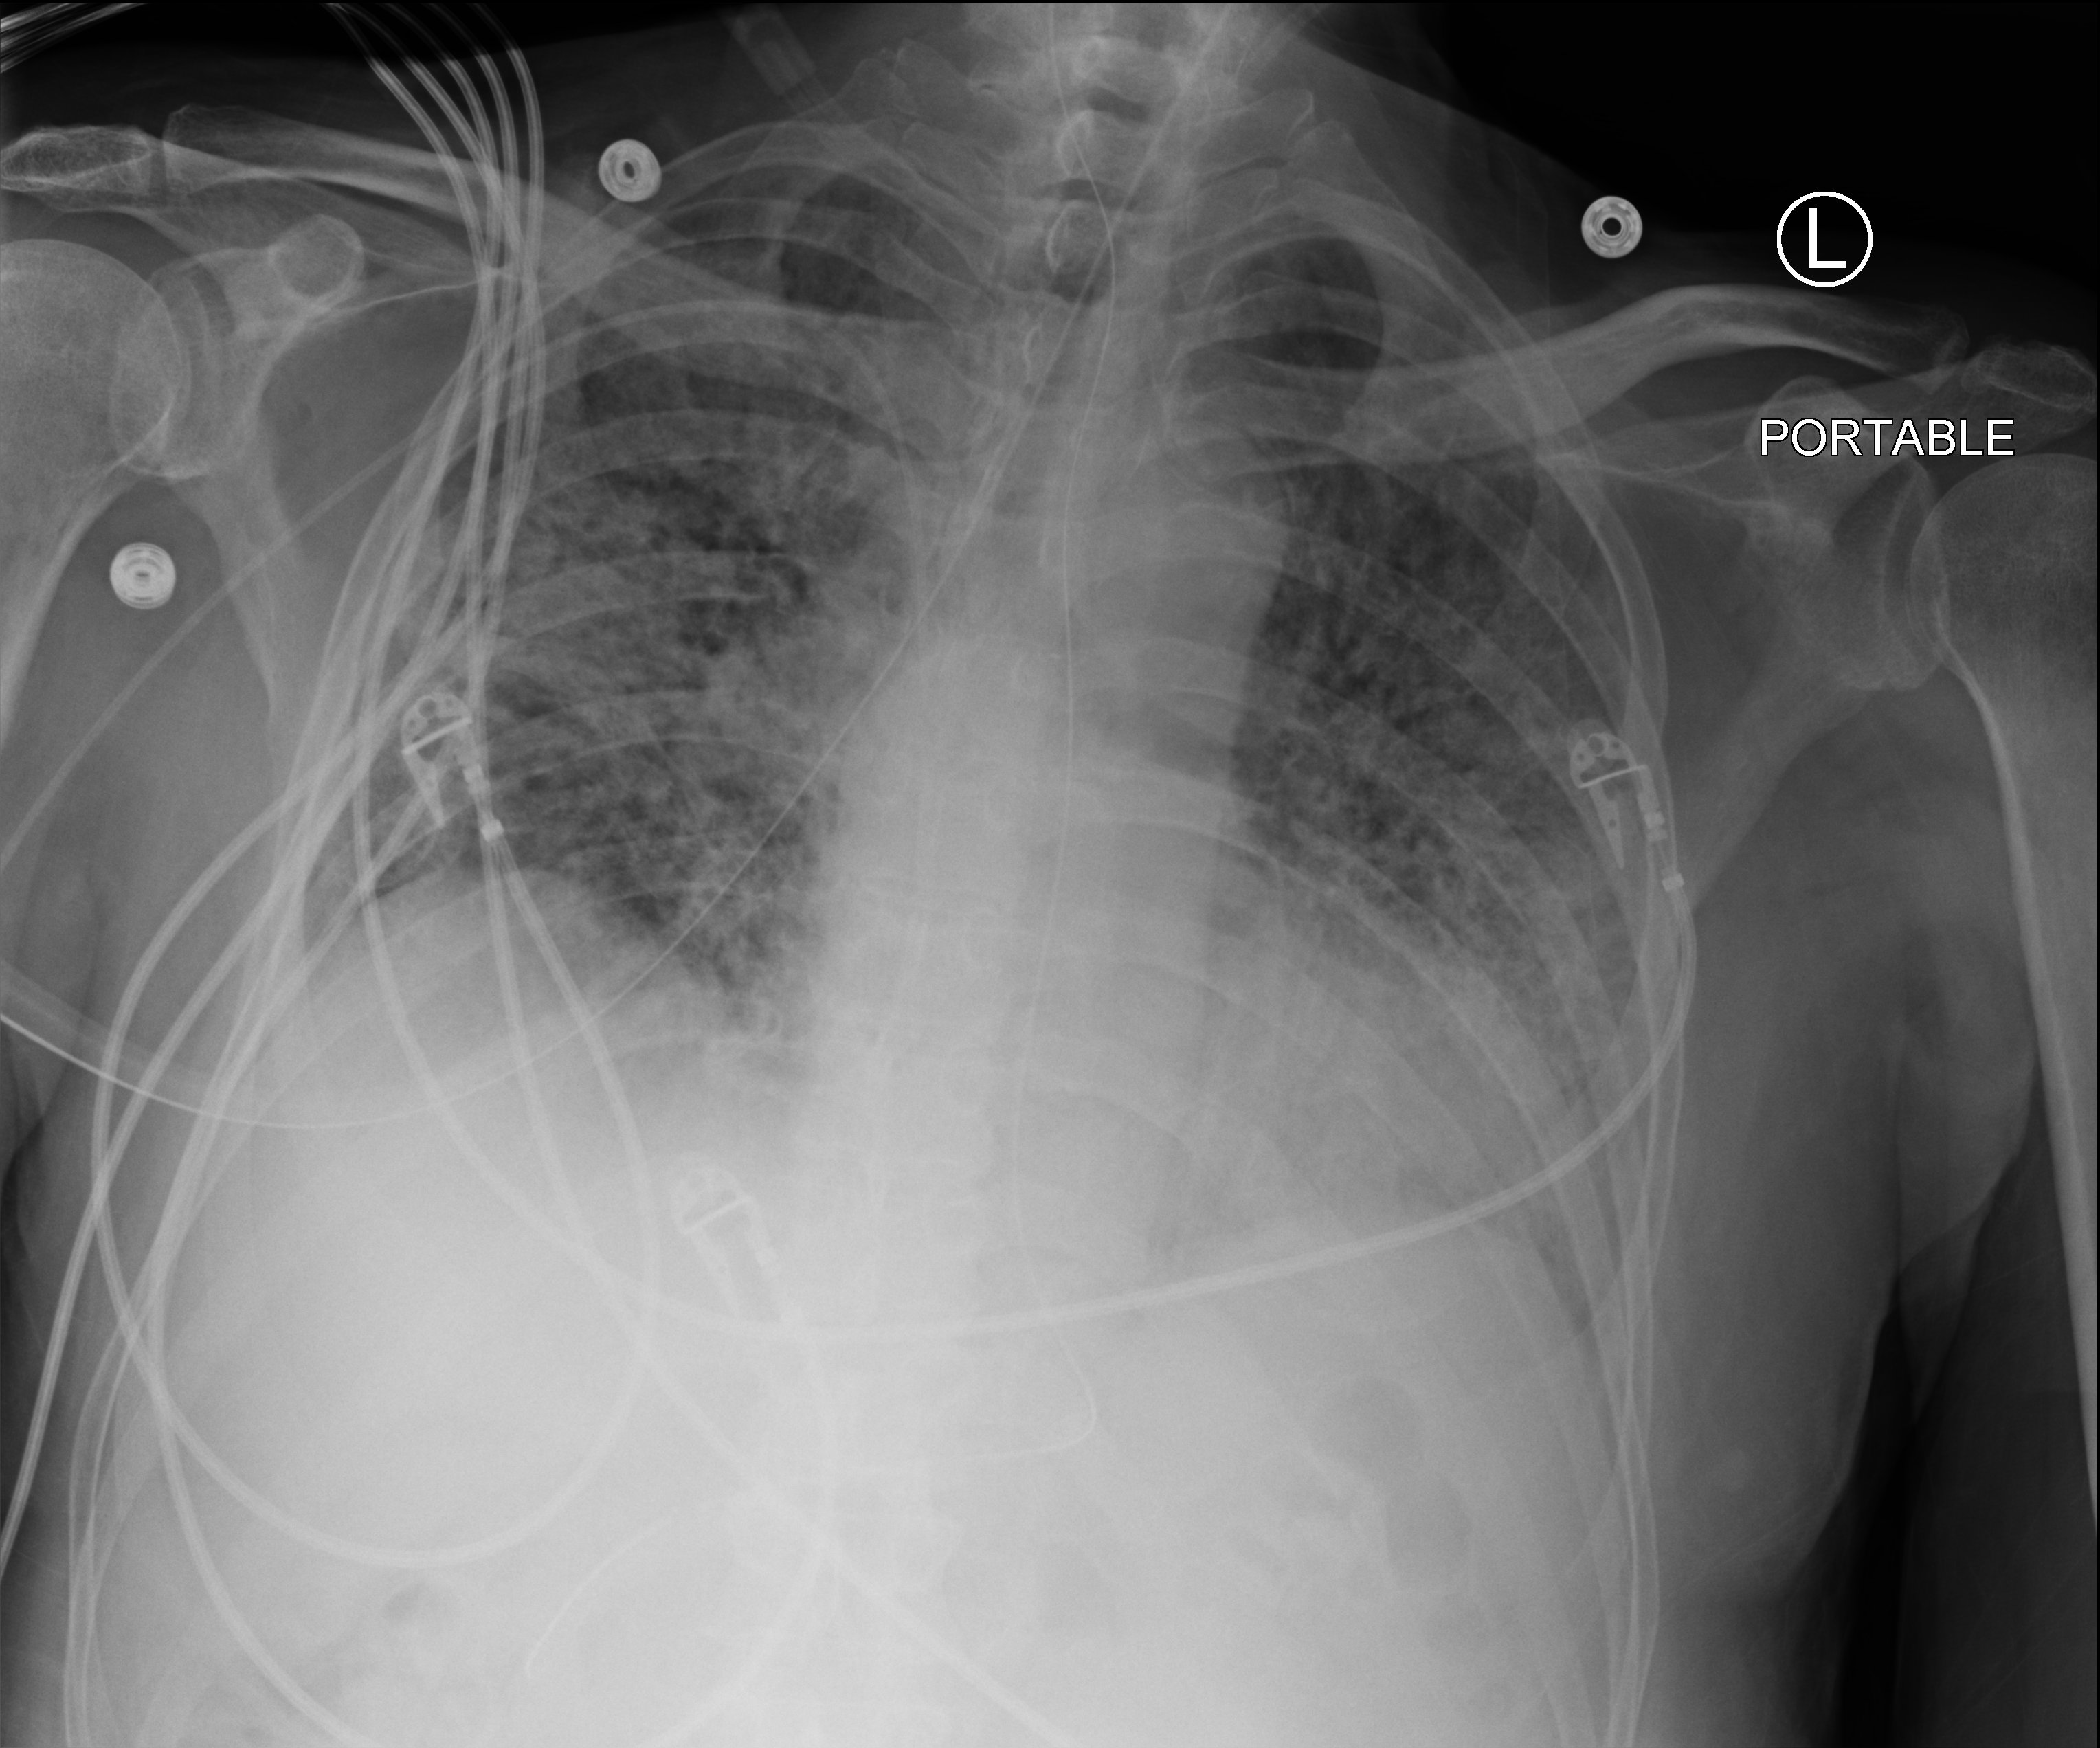
Bedside chest radiograph (computed radiography). Patient hospitalised with COVID-19; male, aged 60–74 years.
From the hospital-stay record, not from the radiograph (when in the stay this image was taken is not recorded): admitted to intensive care during this hospital stay: yes.